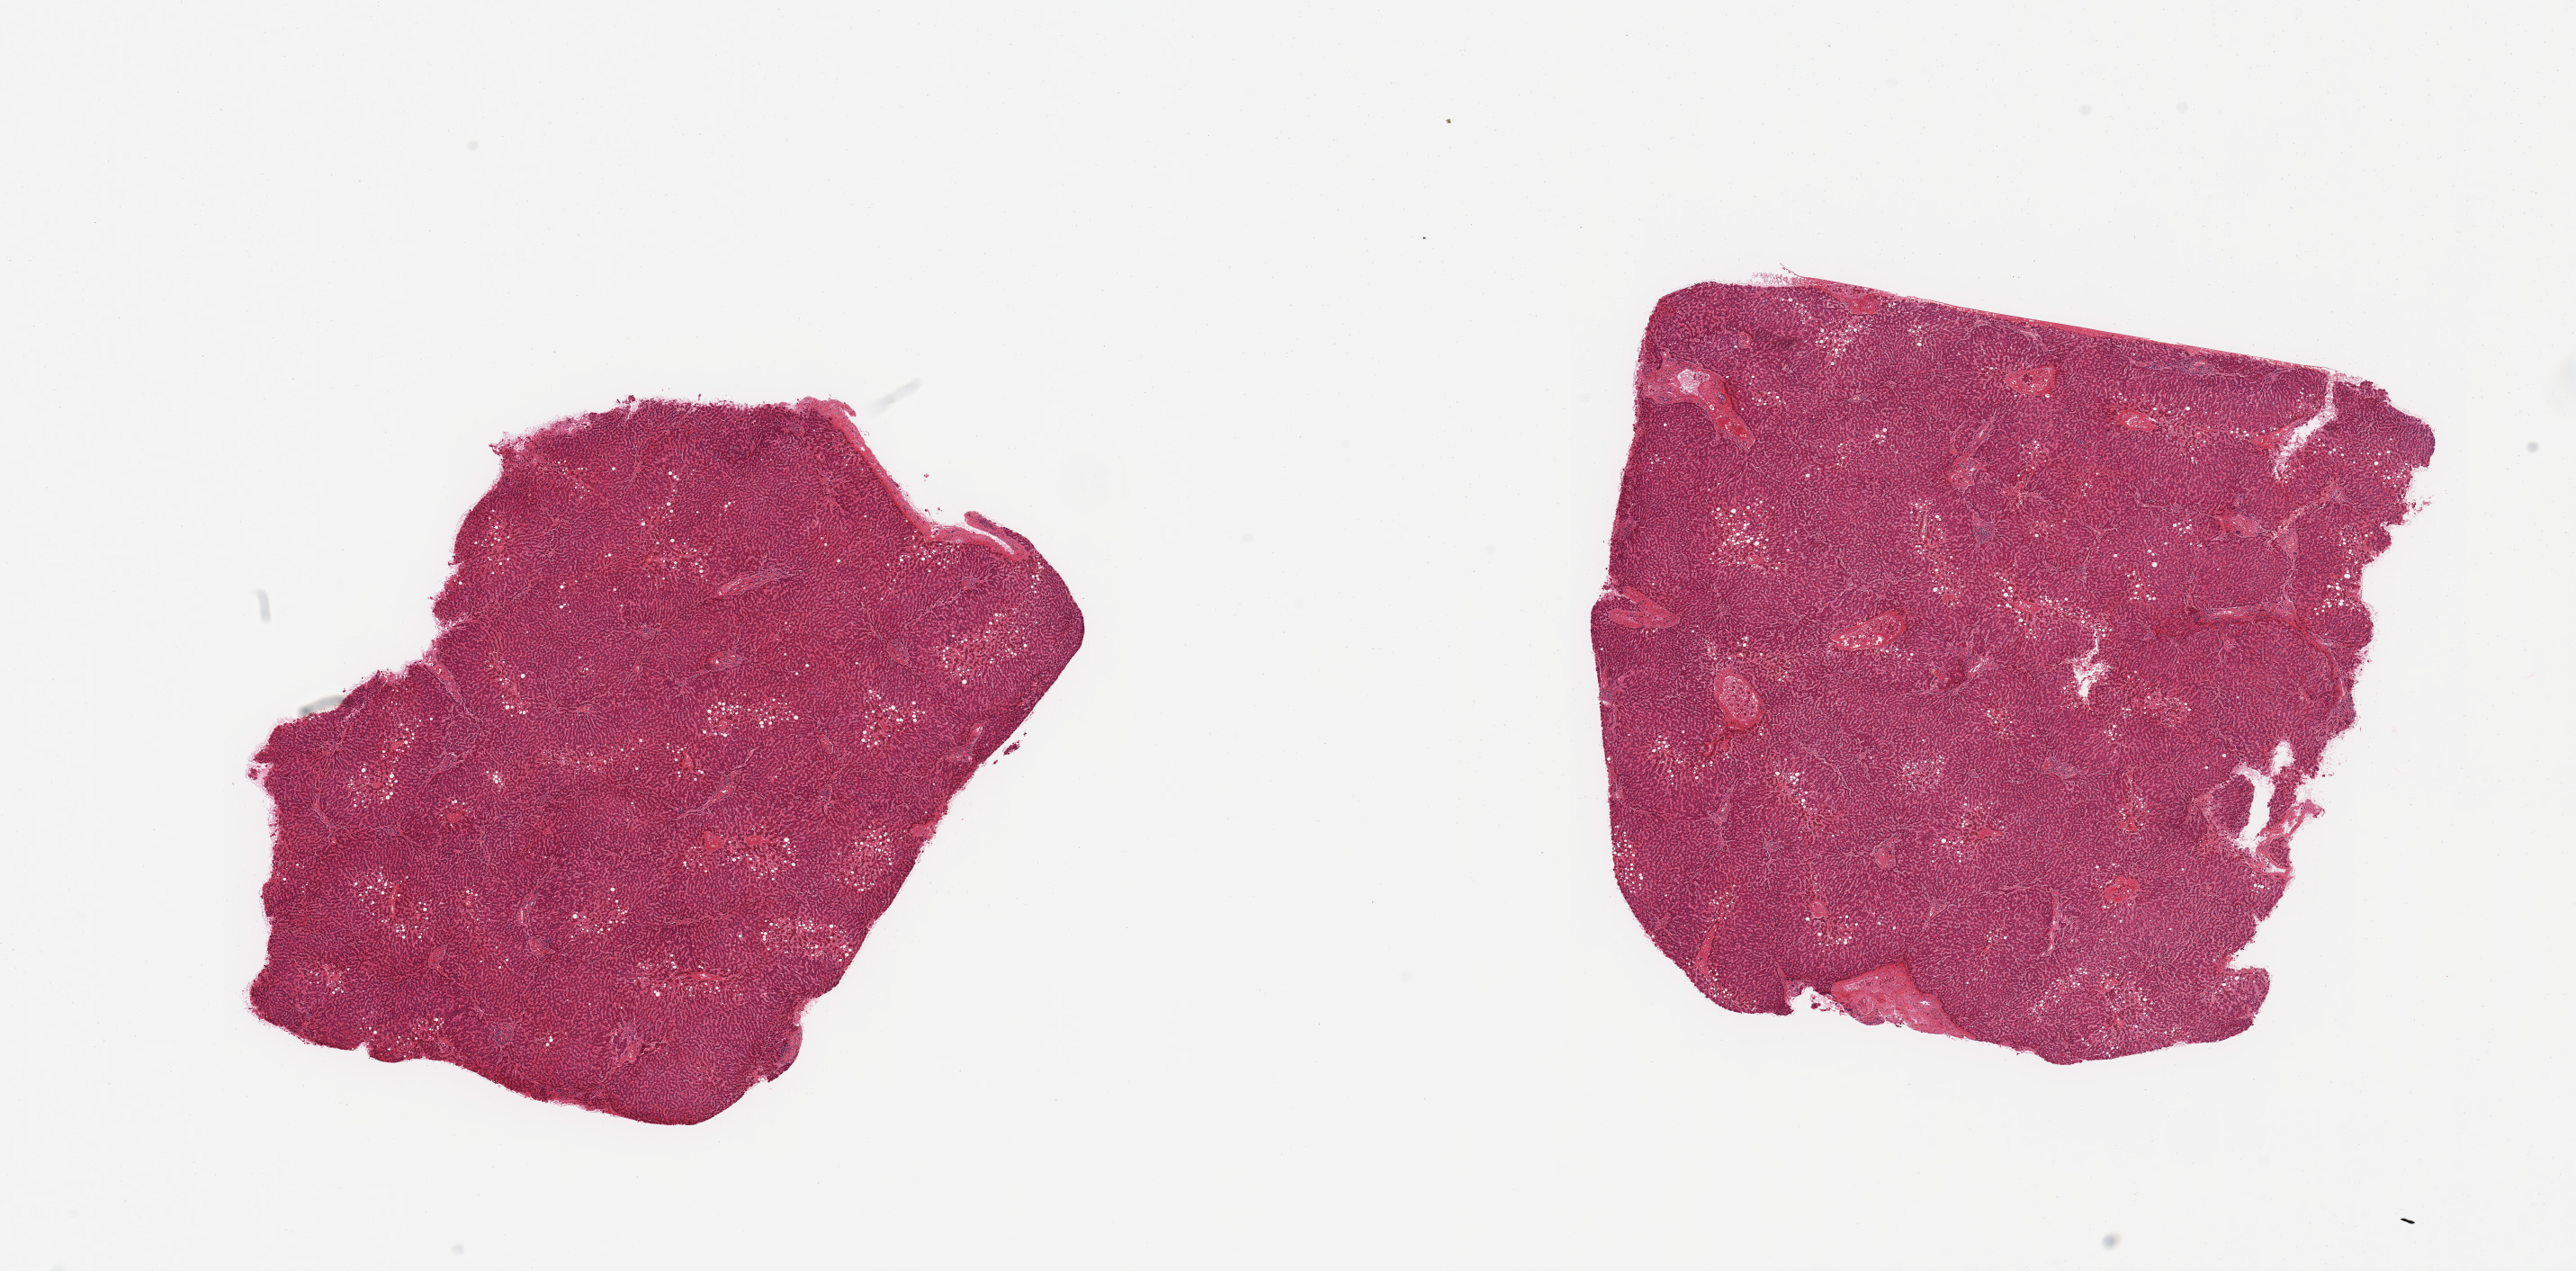
H&E whole-slide image — low-resolution overview of the scanned area, about 22.6 x 11.2 mm (slide scanned at 20x), PAXgene-fixed, paraffin-embedded tissue, sampled site (target tissue): liver, donor tissue sample. Donor: male.
Pathologist's review note for this sample: 2 pieces; congestion and mild steatosis, includes portion of capsule (not target).